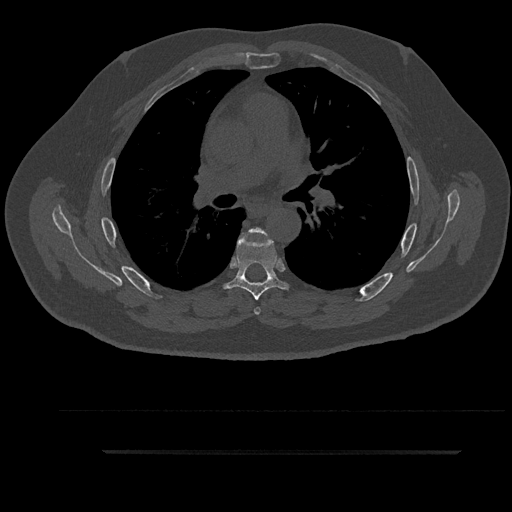
CT including the spine, one axial slice. Slice 586 of 797 in the series (ordered by position). Bone window (W 1800 / L 400 HU). 0.5 mm slice thickness. 512 × 512 image matrix. Male patient, age 63 years. Case-level facts recorded for this patient, not image findings: primary cancer: renal.
Outlined on this slice (semi-automatic segmentation, software-assisted and operator-edited):
- T5 vertebra: bounding box <242,228,268,315> (left, top, right, bottom; pixels)
- T6 vertebra: <224,232,289,301>